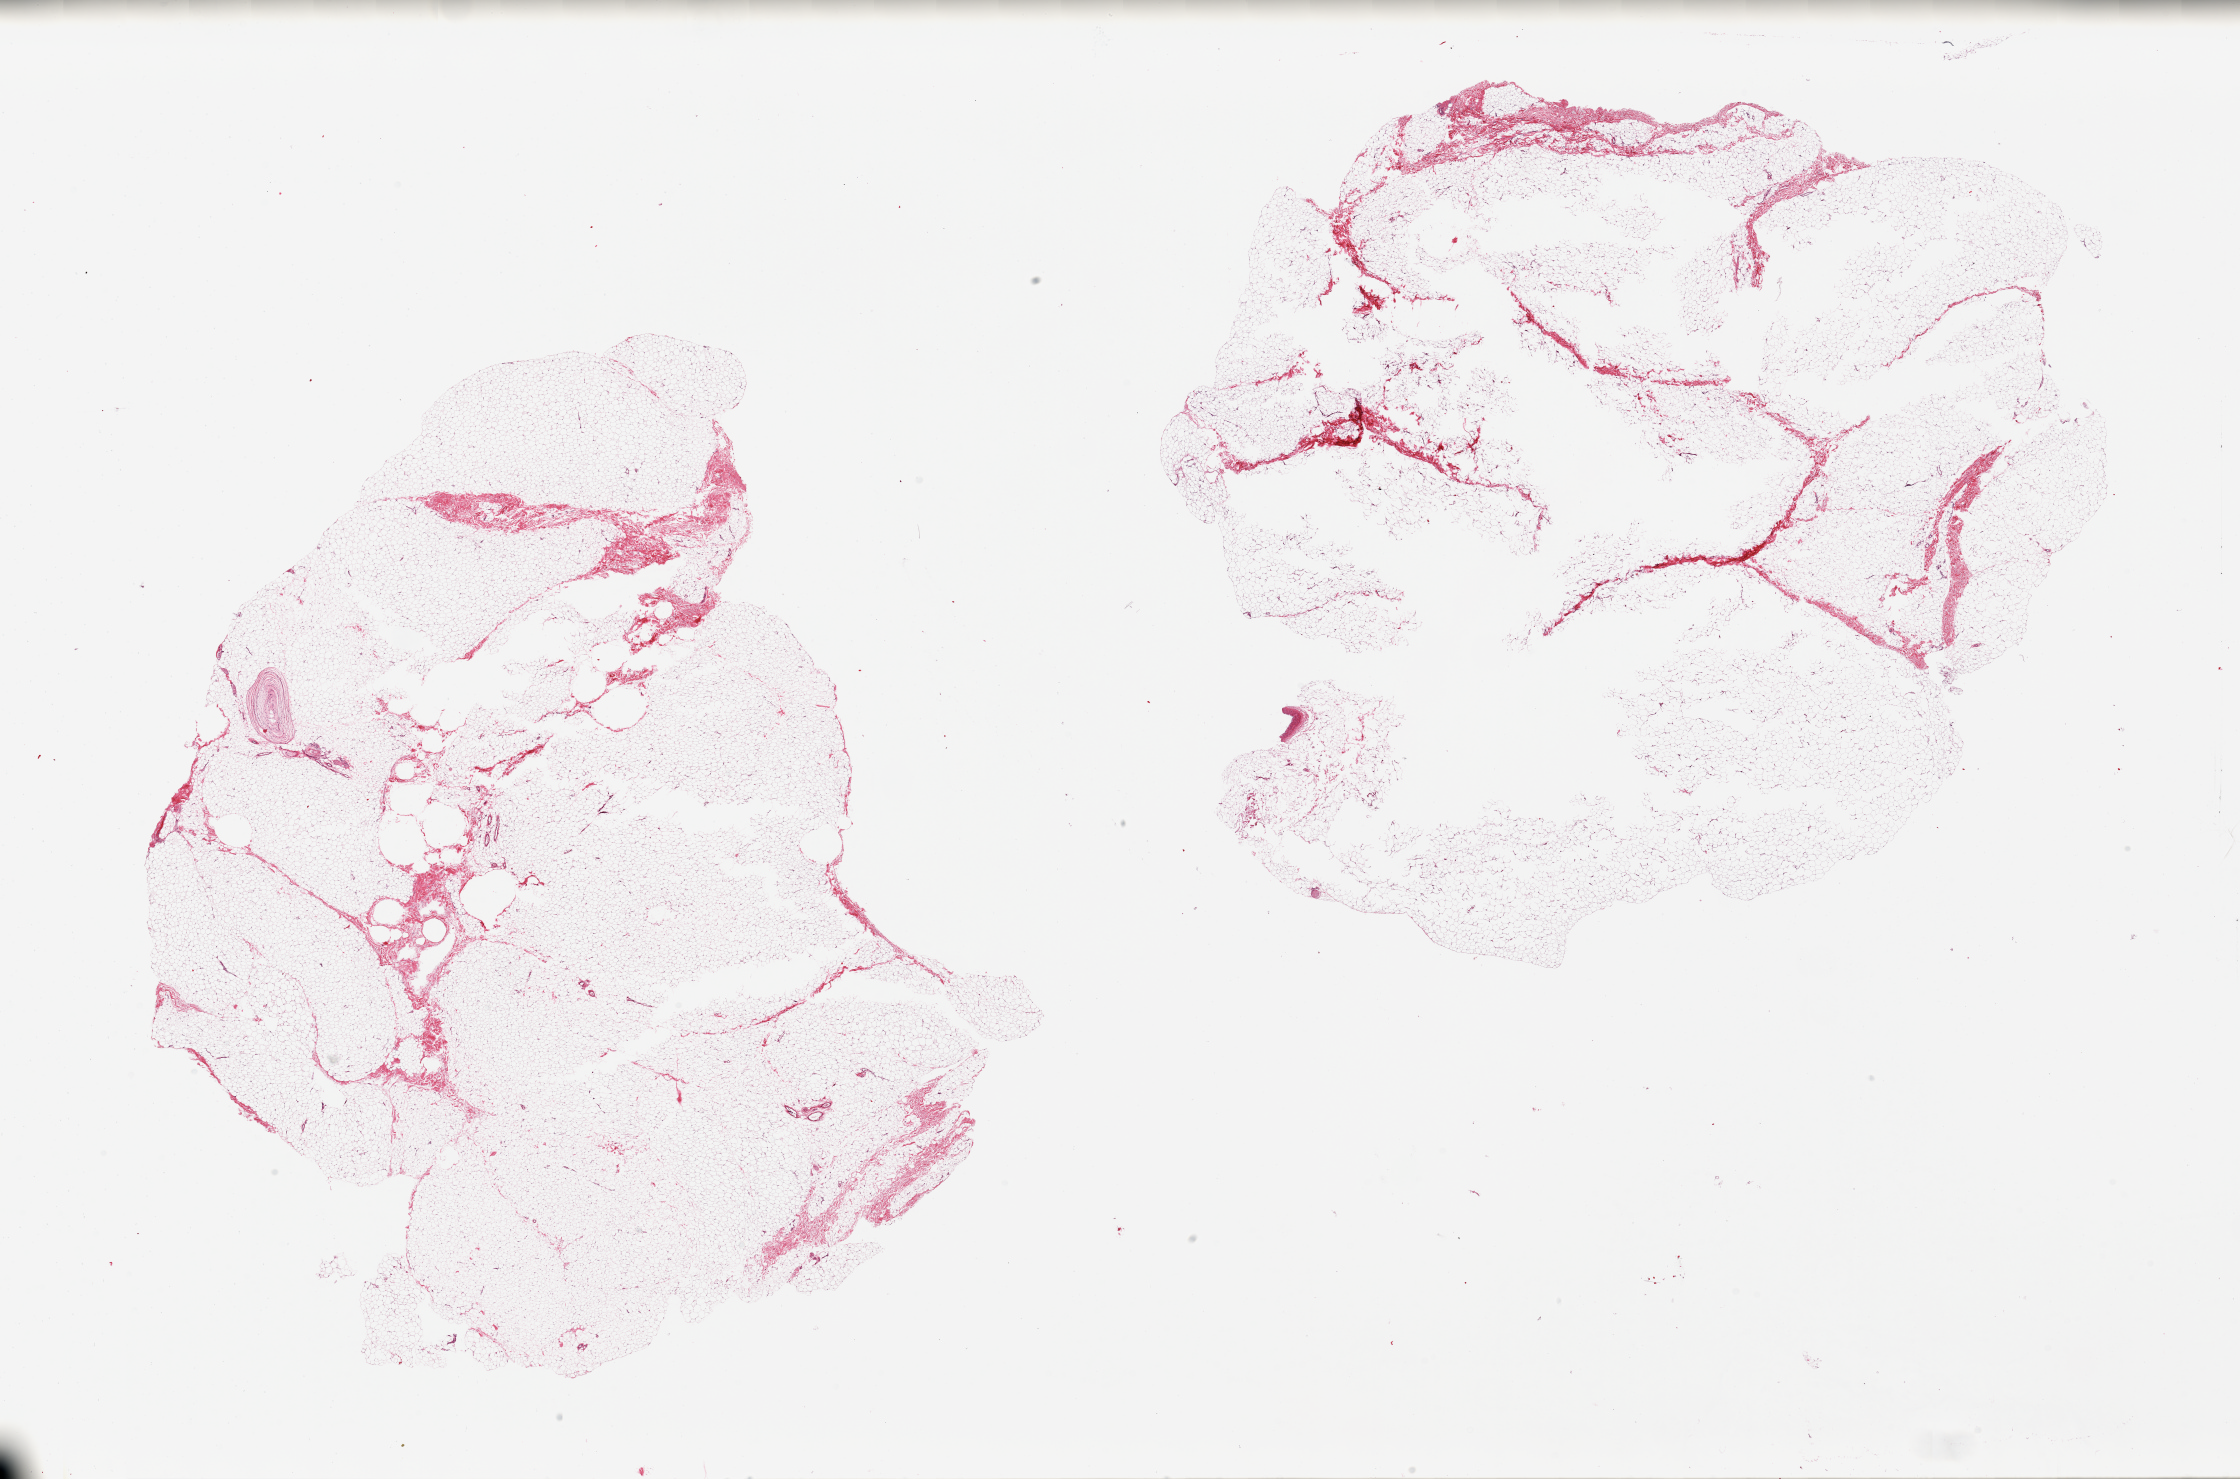
Whole-slide image, hematoxylin and eosin (H&E) stain, shown as a low-resolution overview of the whole scanned area (about 35.4 x 23.4 mm). PAXgene-fixed paraffin-embedded (PFPE) section. Target tissue: breast. Donor tissue sample. Donor sex: male.
- review note (as recorded): 2 pieces with internal holes; All largely fatty without mammary ducts